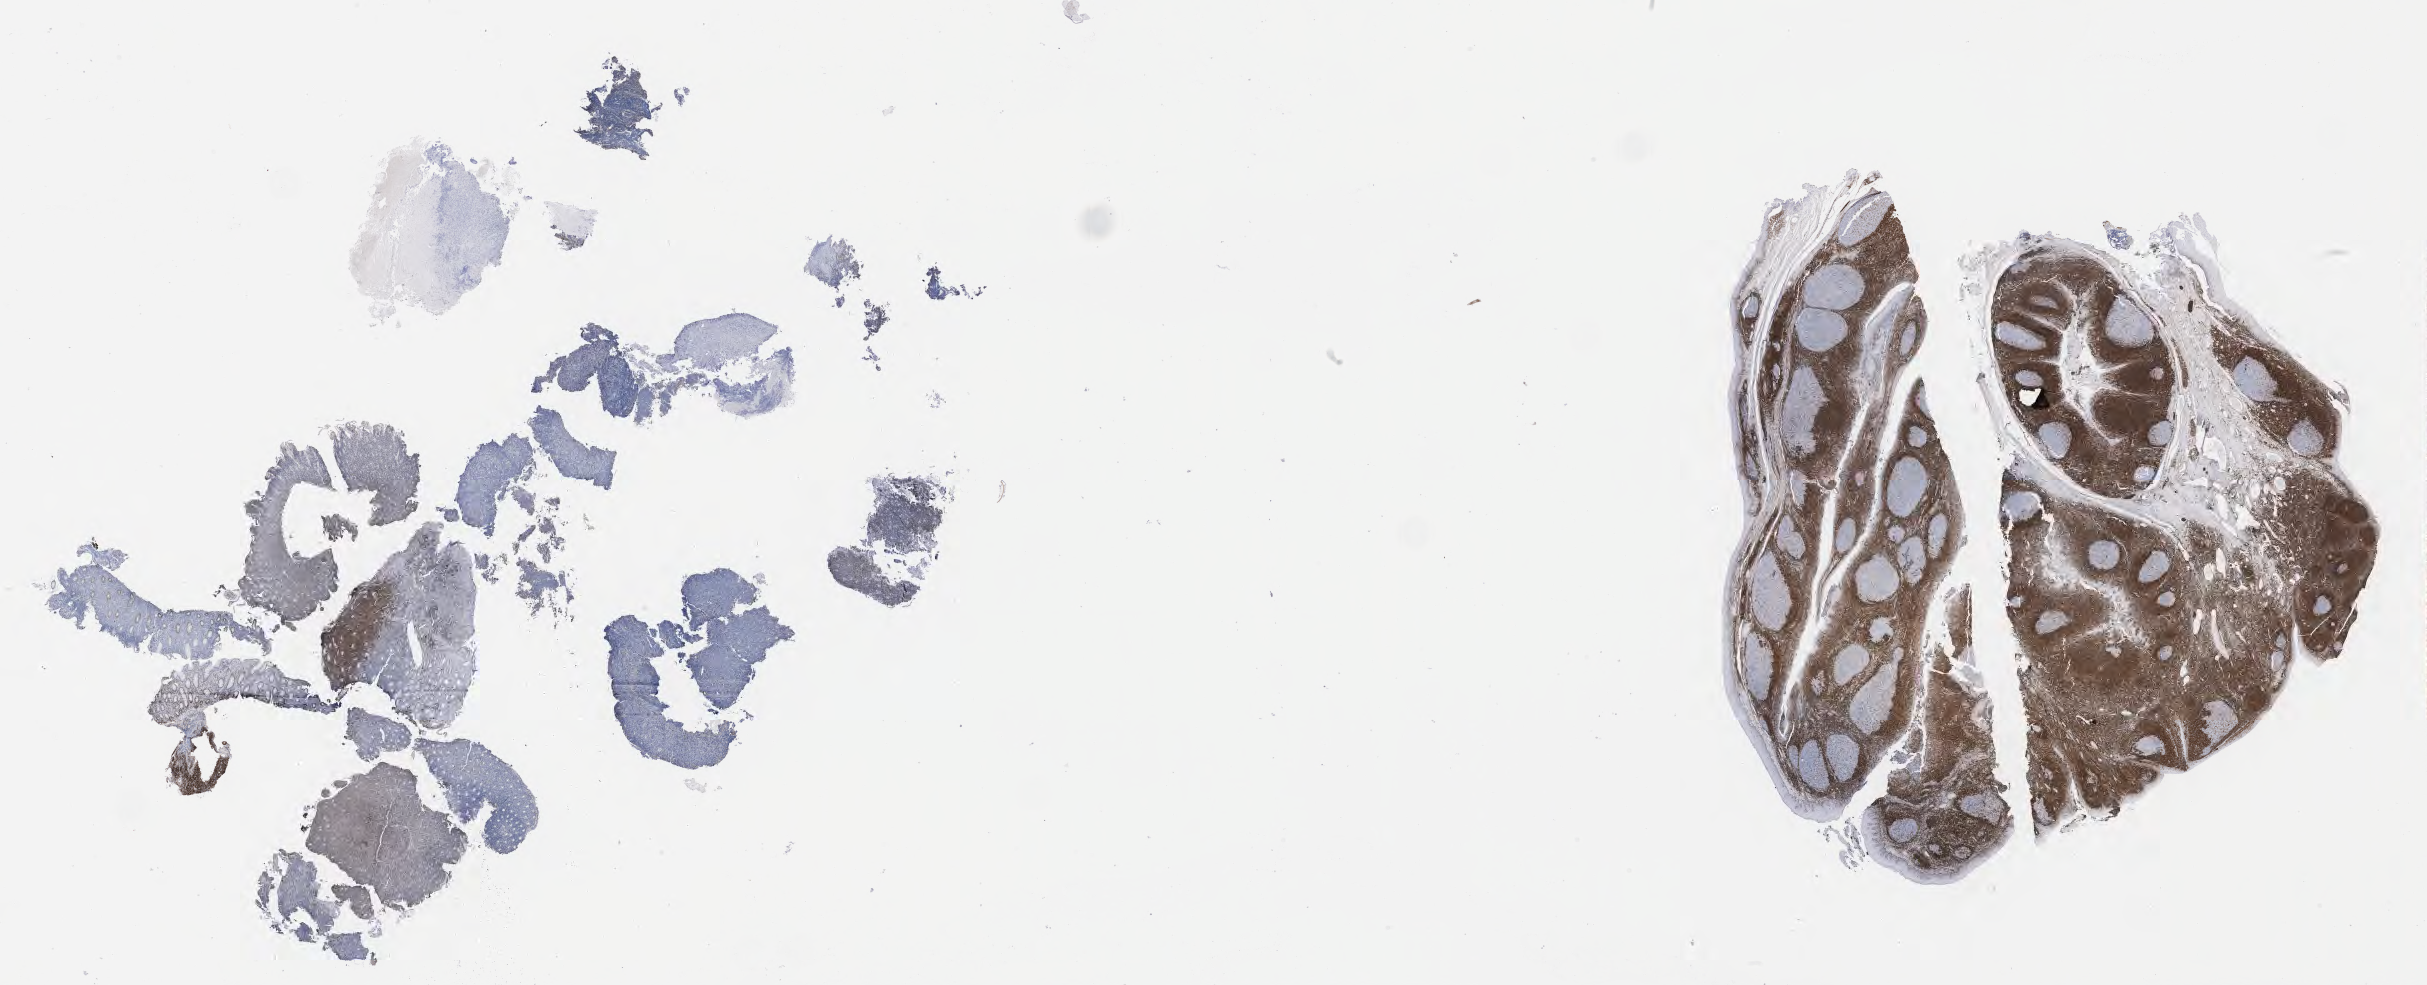
Immunohistochemistry (IHC) whole-slide image stained for BCL2, whole scanned area (about 39.2 x 15.9 mm) shown as a low-resolution overview, tumor tissue. Patient male; aged 56.
Histologic diagnosis: Burkitt lymphoma, NOS.